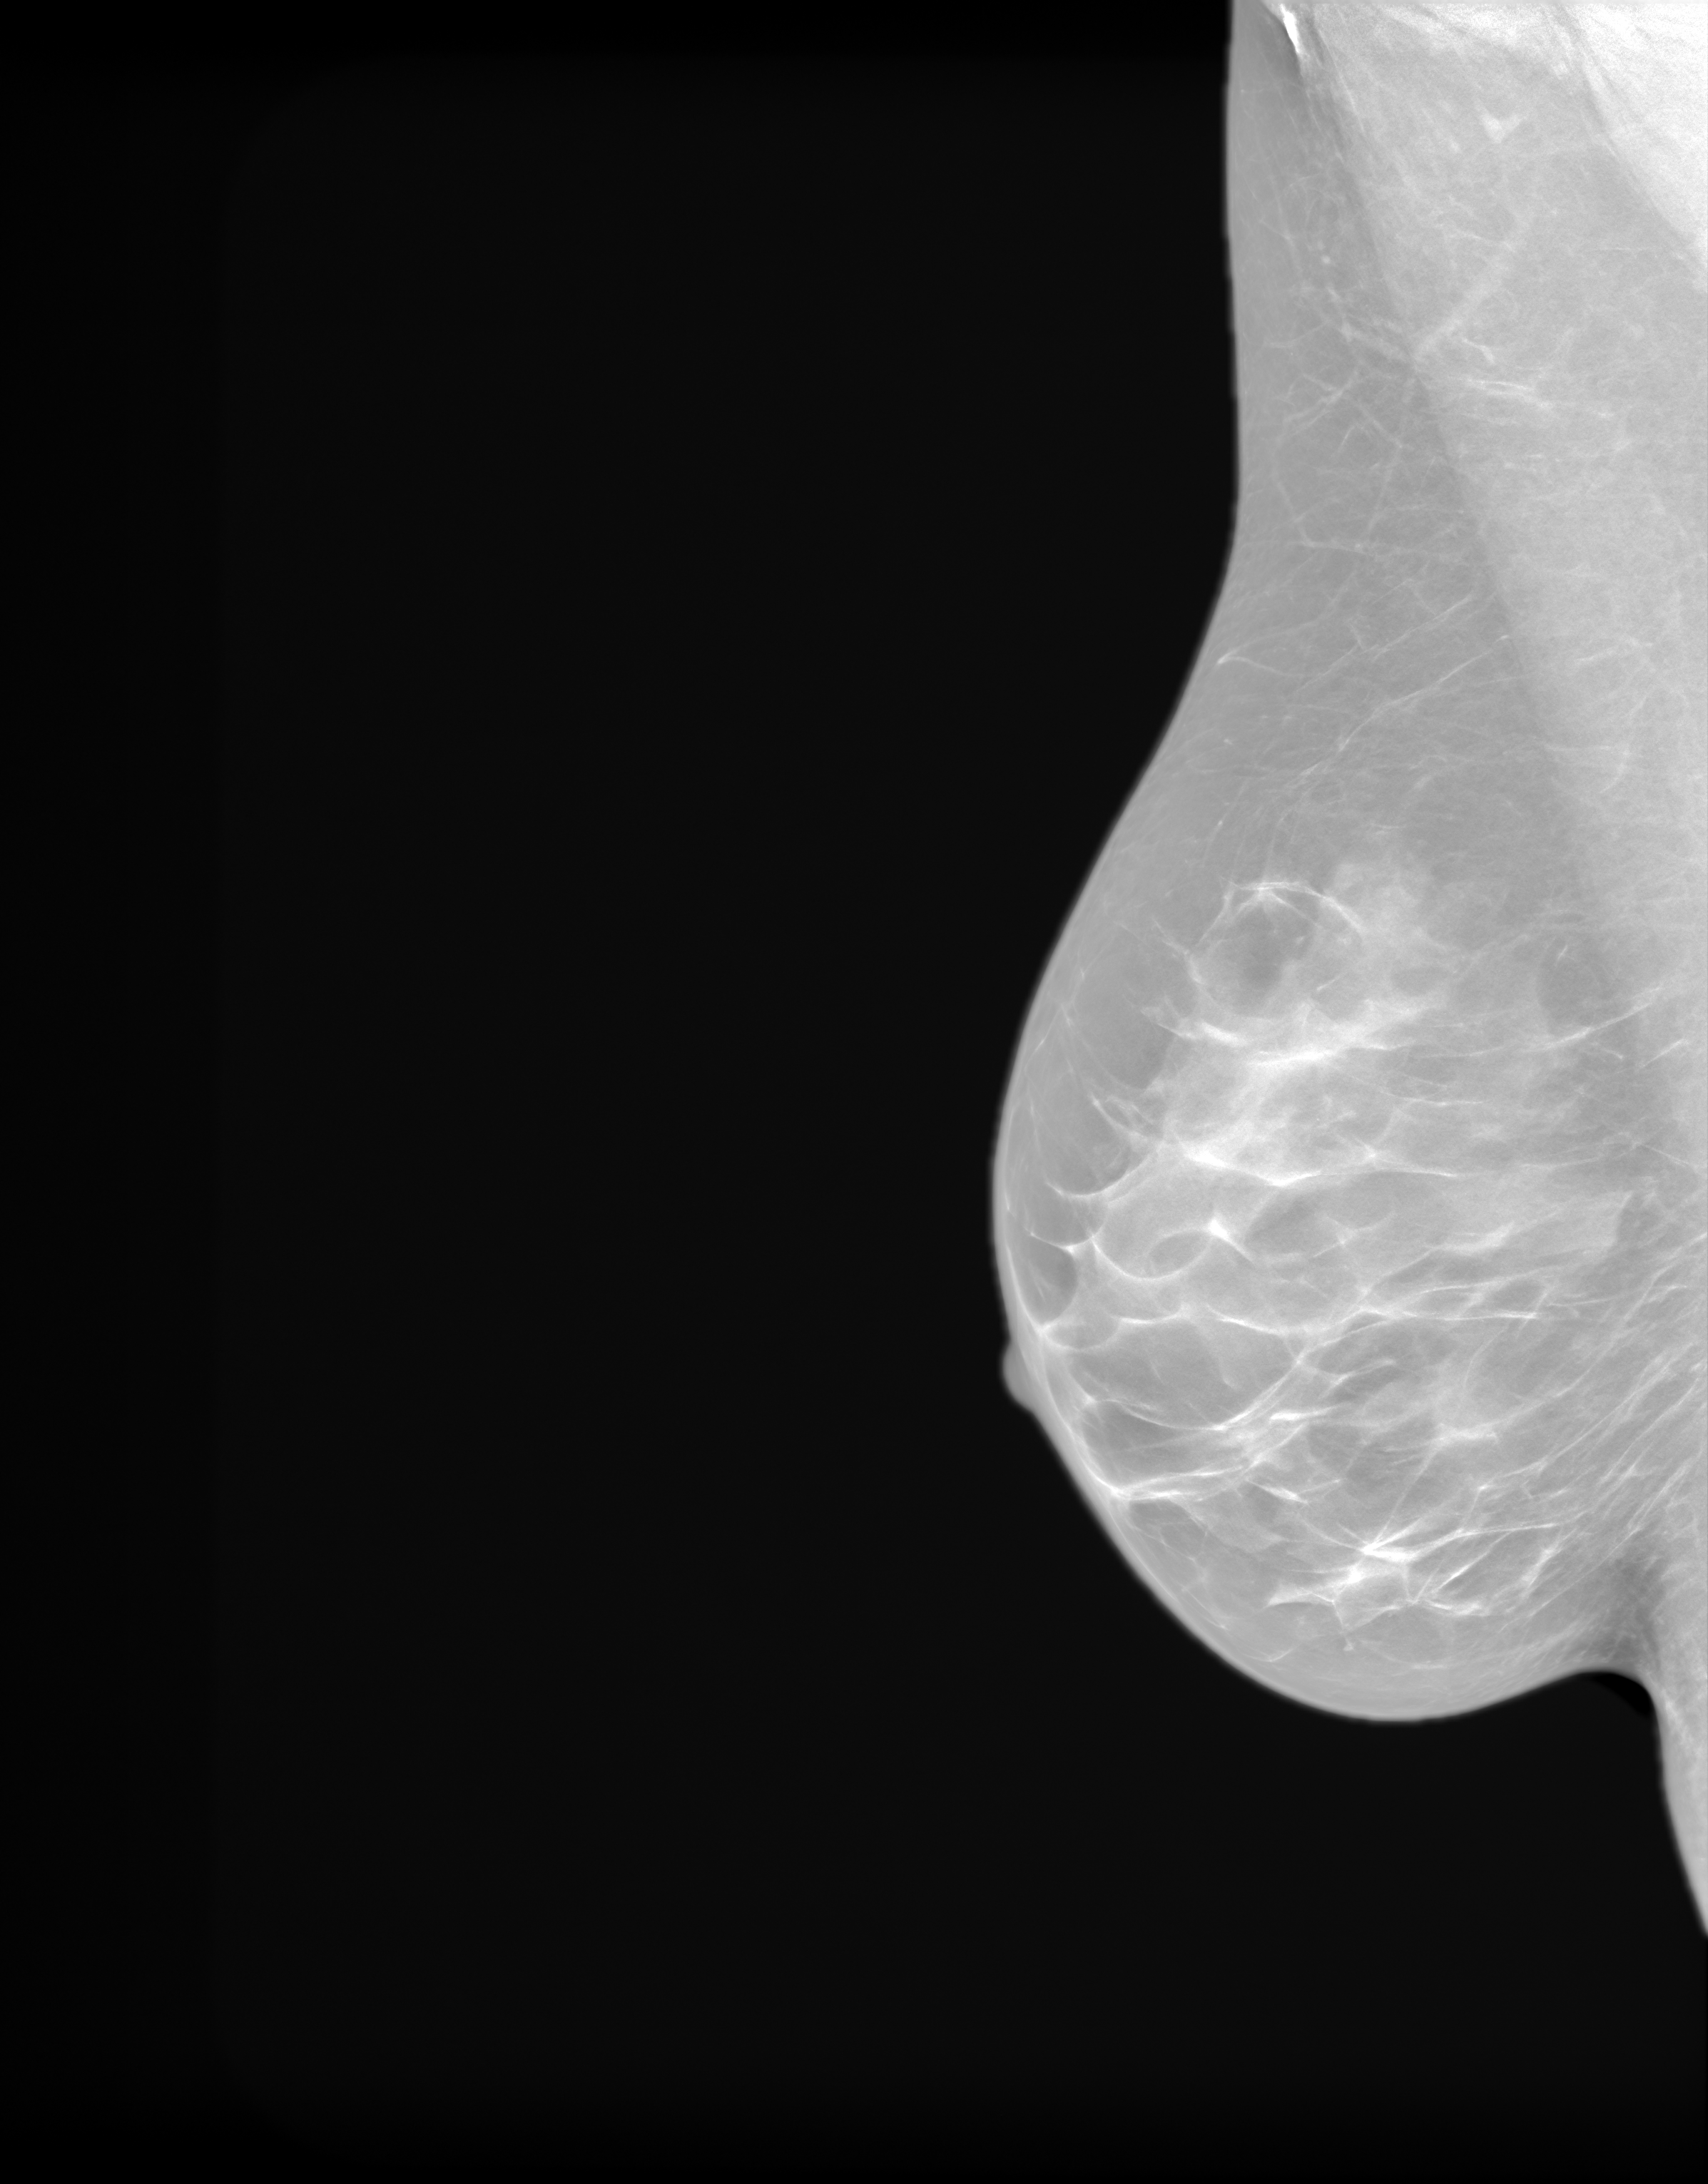
Annual screening mammography examination. Female patient, age 52 years.
Image type: synthesized 2-D view from tomosynthesis. Breast: right. Projection: medio-lateral oblique projection.